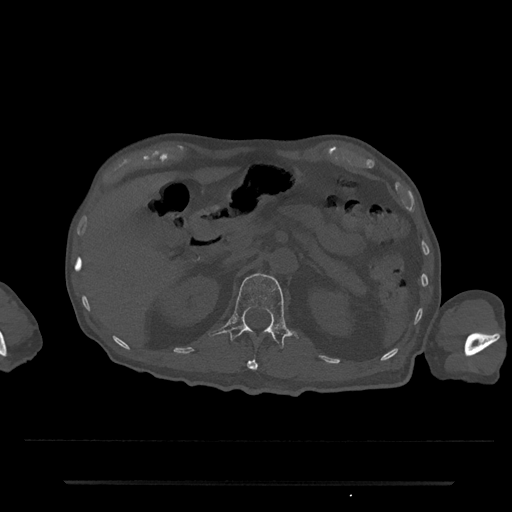
CT including the spine, one axial slice. Slice 145 of 797 in the series (ordered by position). Reconstruction kernel Br40s/3. Bone window (W 1800 / L 400 HU). 0.5 mm slice thickness. 512 × 512 image matrix, field of view 427 × 427 mm. Patient: male, 74 years. From the clinical record (not read from this slice): primary cancer: prostate.
Outlined on this slice (semi-automatic segmentation, software-assisted and operator-edited):
- L1 vertebra: bounding box <210,273,295,349> (left, top, right, bottom; pixels)
- T12 vertebra: <247,358,258,370>